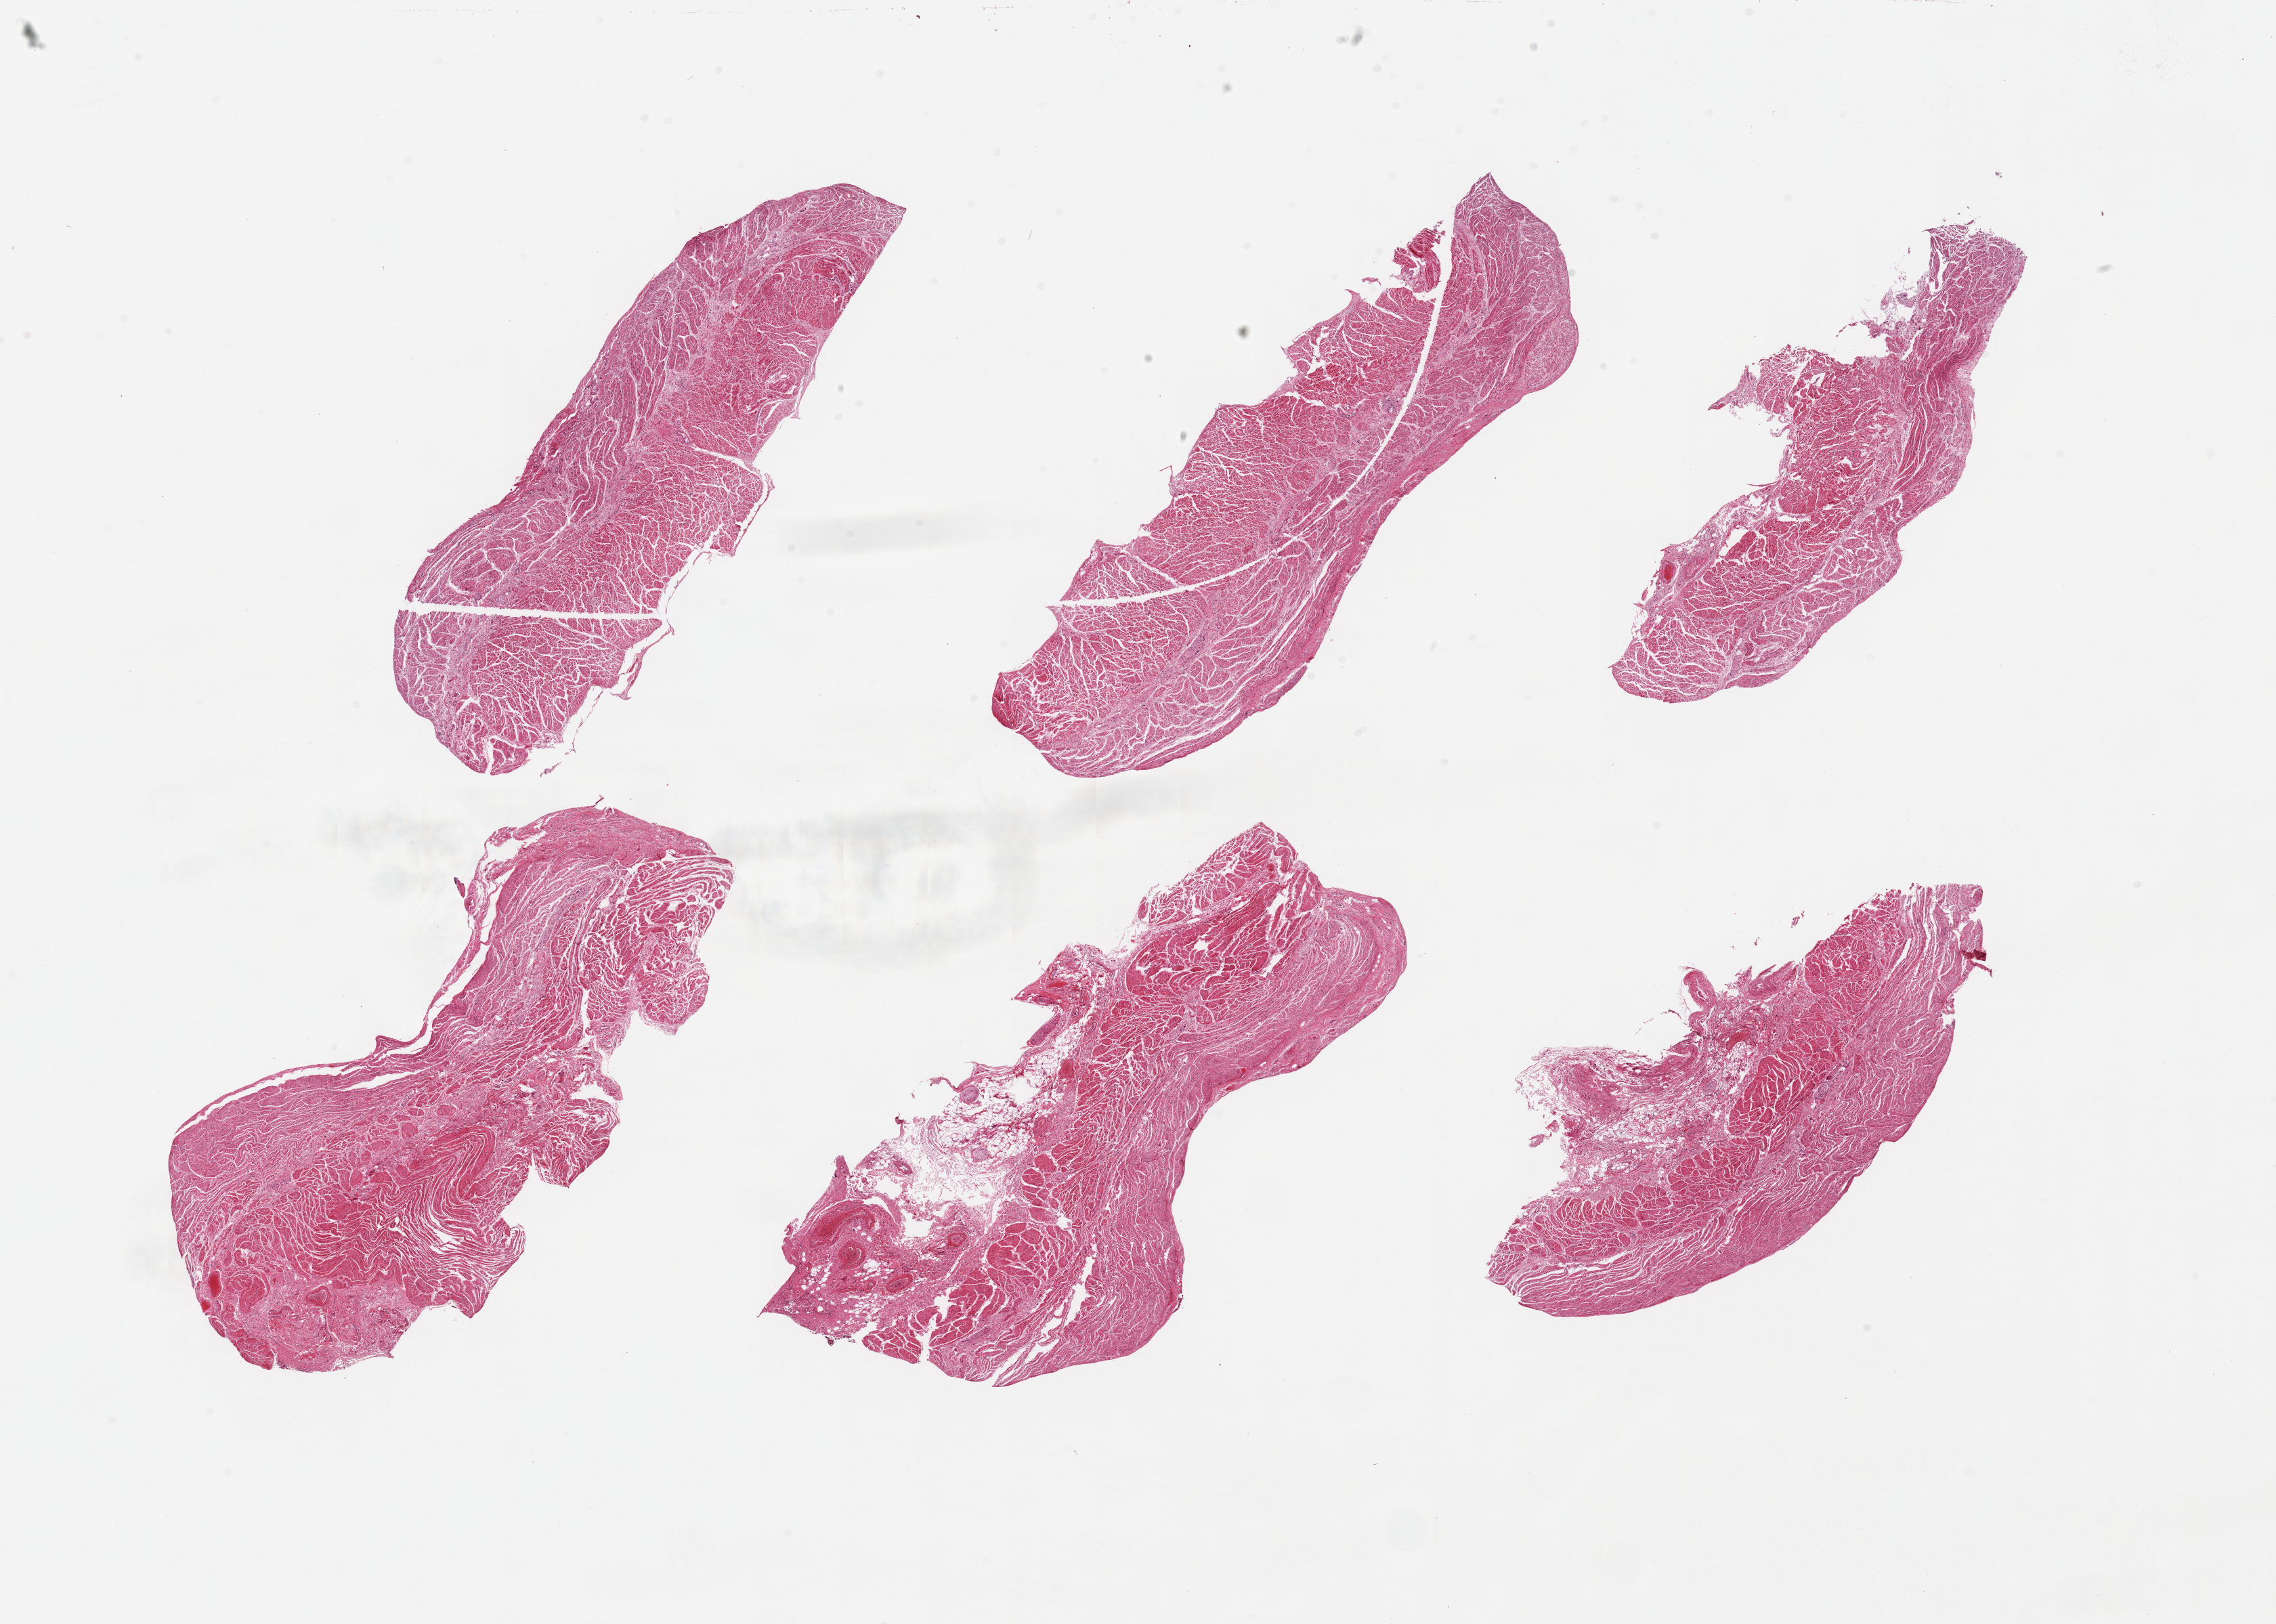
Whole-slide image, hematoxylin and eosin (H&E) stain — a low-resolution overview of the entire scanned area, about 26.6 x 19.0 mm (slide scanned at 20x). PAXgene-fixed paraffin-embedded (PFPE) section. Sampled site (target tissue): gastroesophageal junction. Tissue donor sample. Male donor.
Reviewer comment on this tissue sample: 6 pieces; 1 piece has a 1.2x2.6 mm focus of fat.